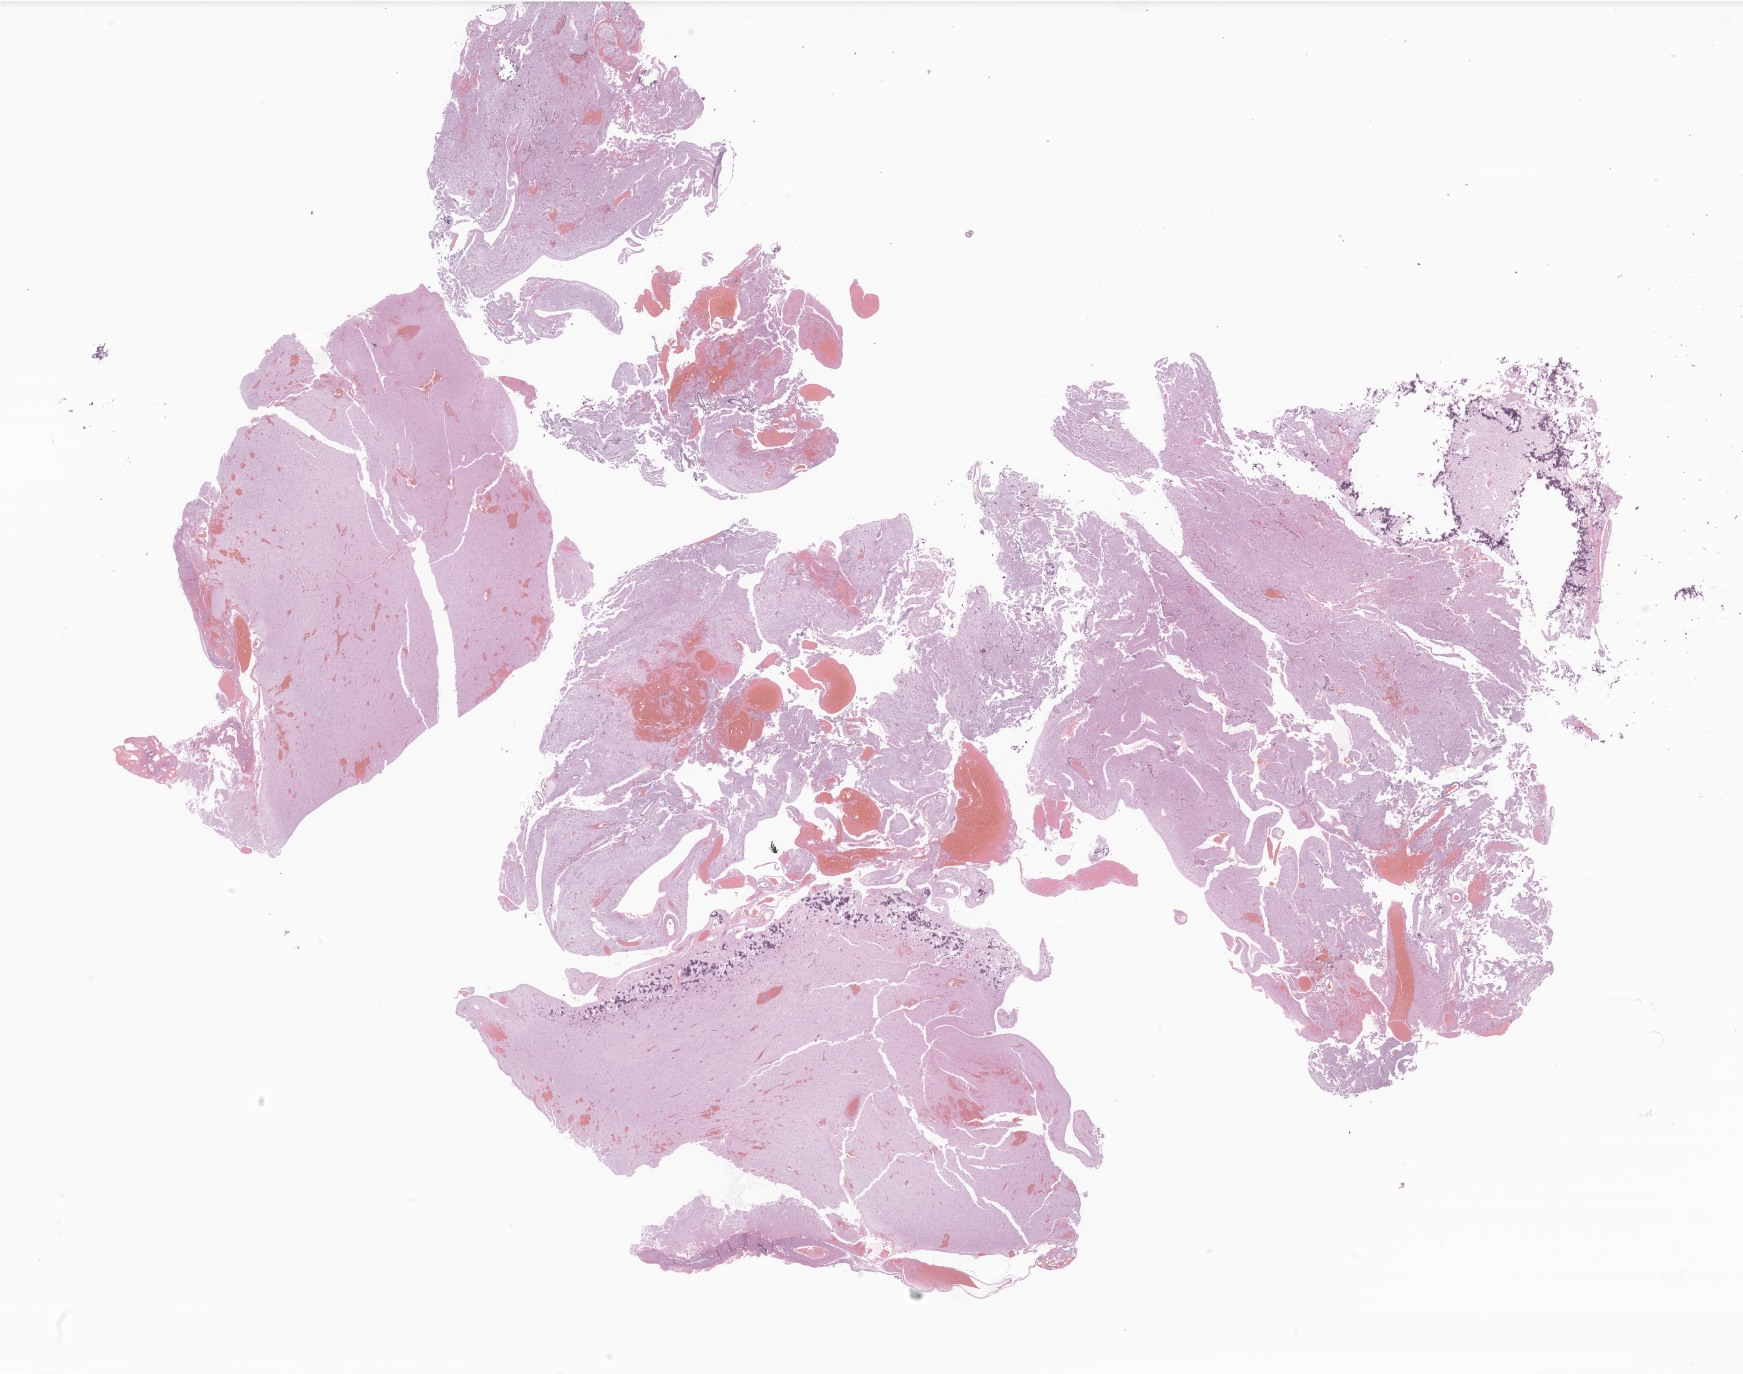
Hematoxylin and eosin (H&E) whole-slide image of tumor tissue from the brain — a low-resolution overview of the entire scanned area, about 29.4 x 23.2 mm; formalin-fixed paraffin-embedded section. Patient male; age 188 months (15 years 8 months).
Diagnosis (ICD-O-3 morphology term): Glioma, malignant.